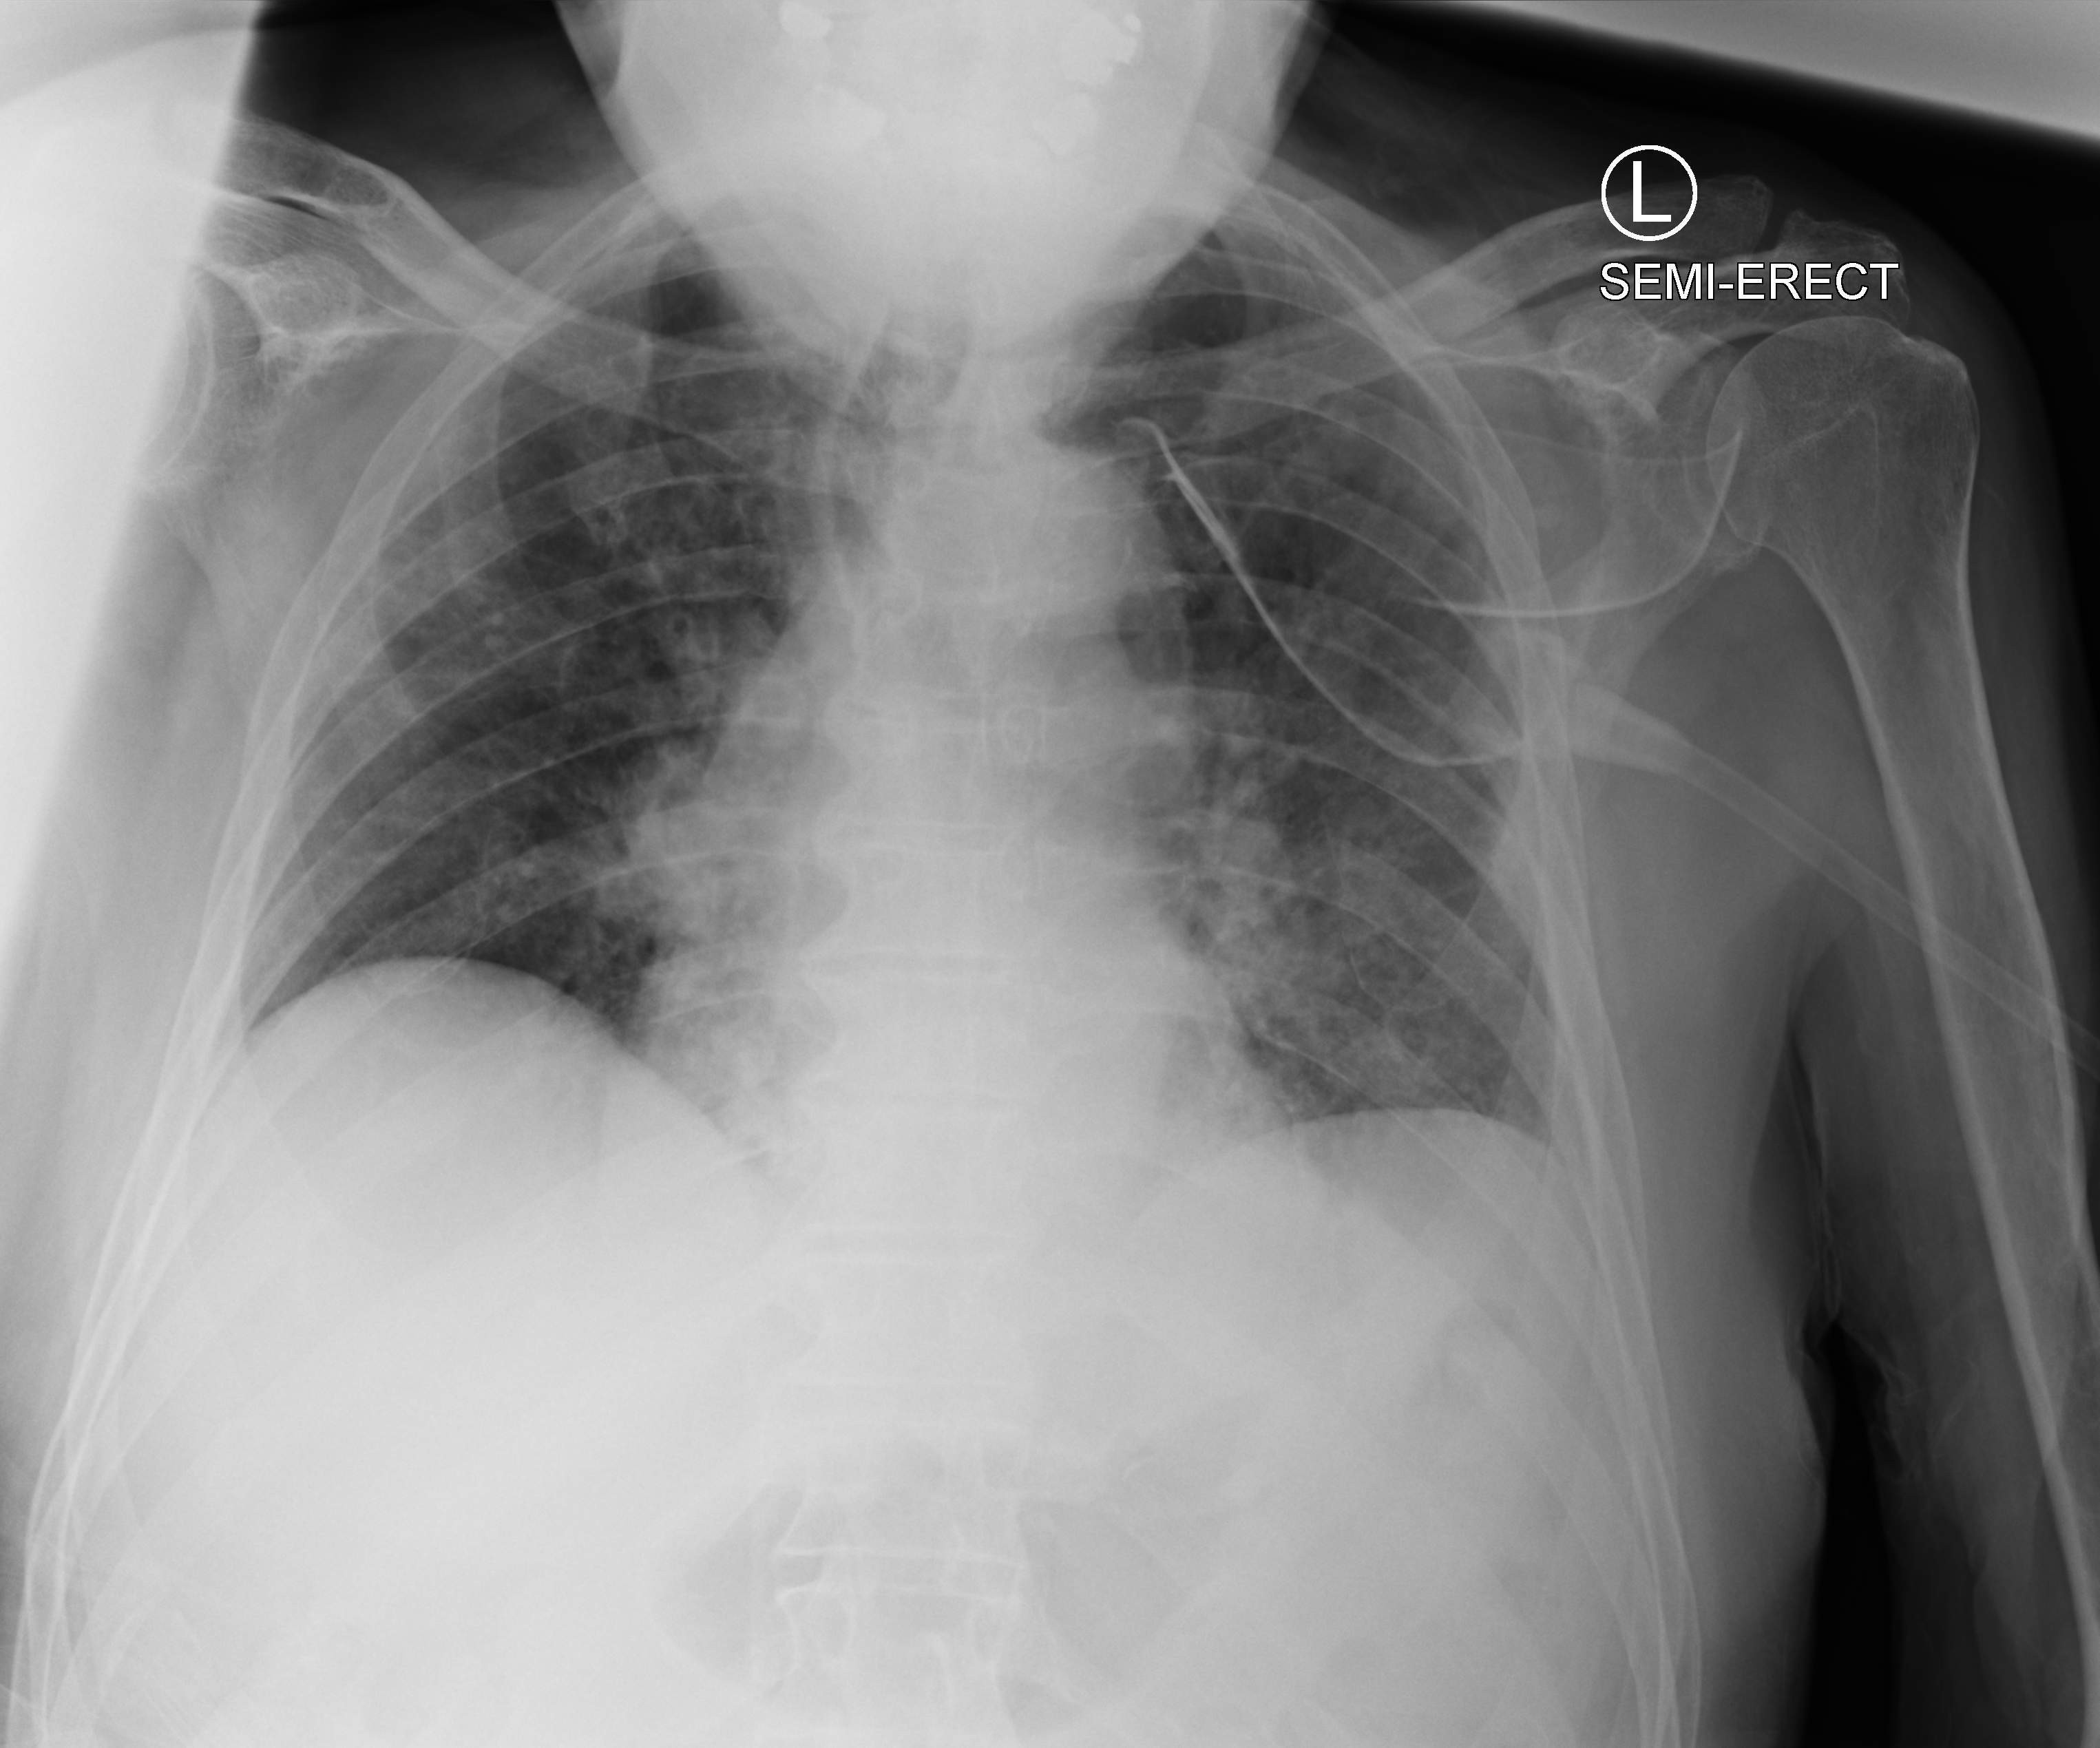
Chest X-ray (portable); anteroposterior (AP) projection. Patient hospitalised with COVID-19; male, aged 75–90 years.
Hospital-stay facts (about this admission, not read from this image; timing relative to this image not recorded): admitted to intensive care during this hospital stay: no.